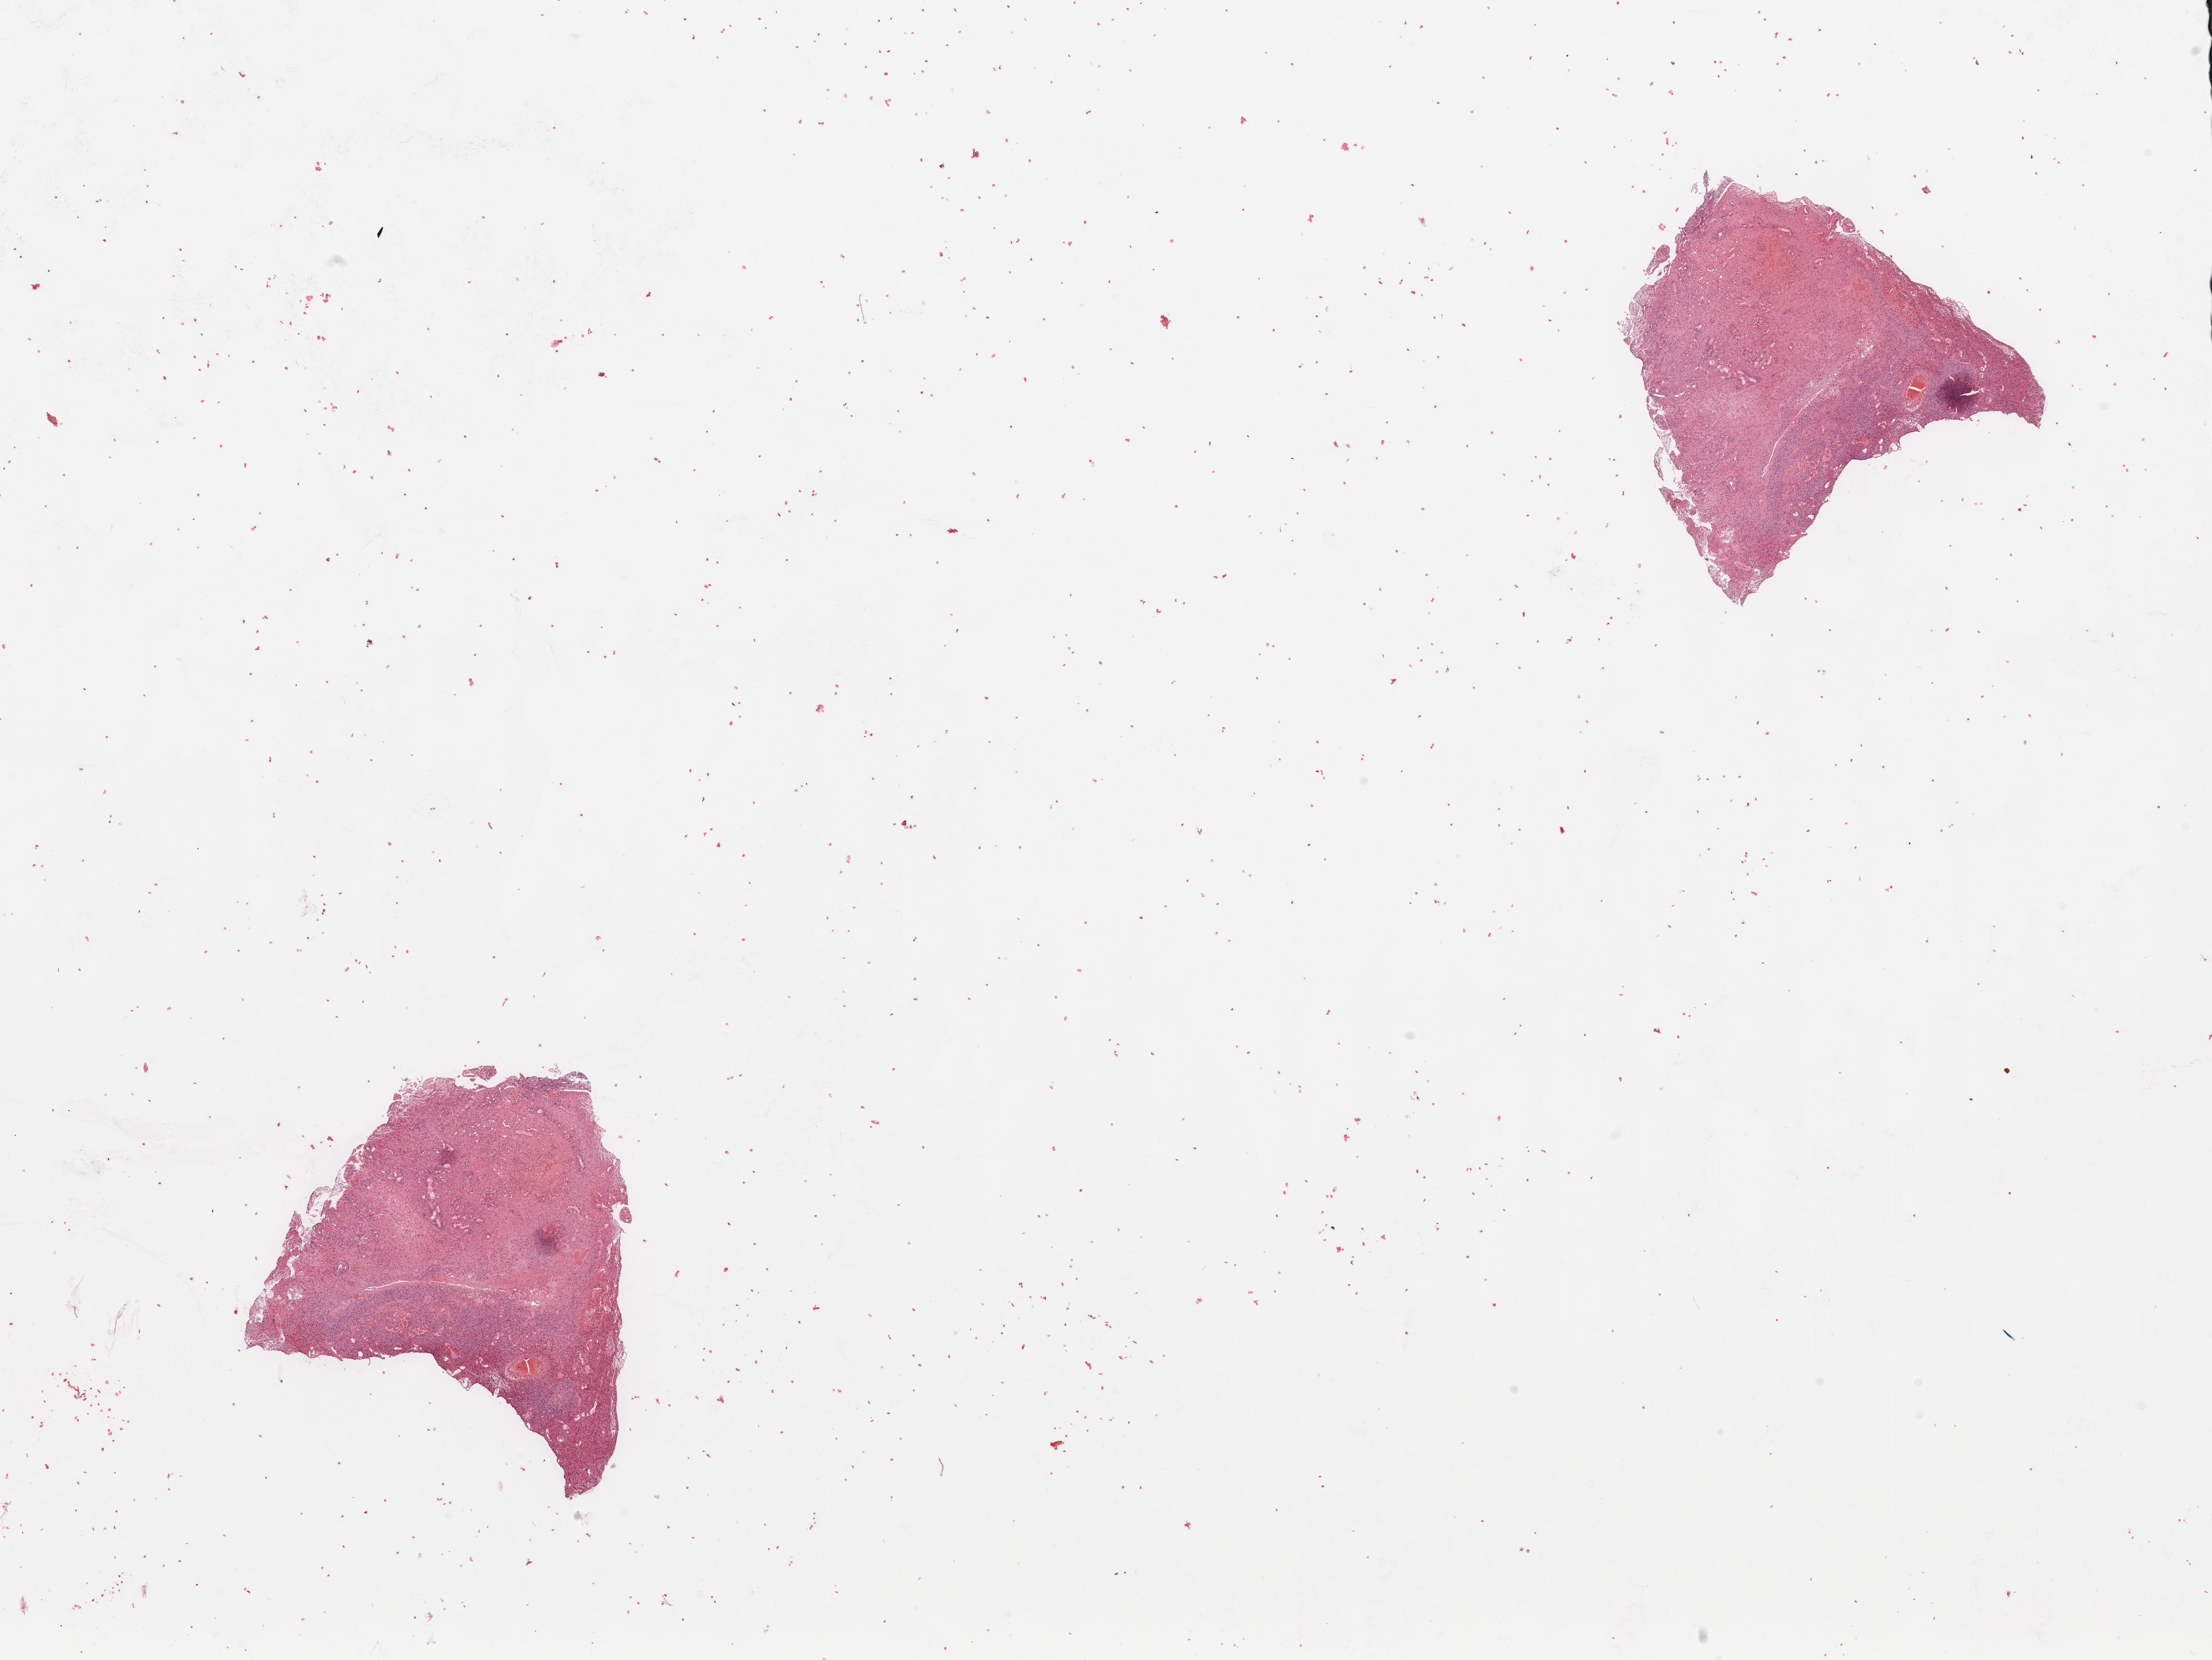
Whole-slide histology image, H&E, a low-resolution overview of the entire scanned area, about 26.6 x 19.9 mm; tumour tissue sample, sampled site: occipital cortex. 64-year-old female patient. Slide review estimates, as recorded: tumour nuclei 65%, necrosis 5%.
Primary tumour site (as recorded): occipital lobe. Histologic diagnosis: Glioblastoma.